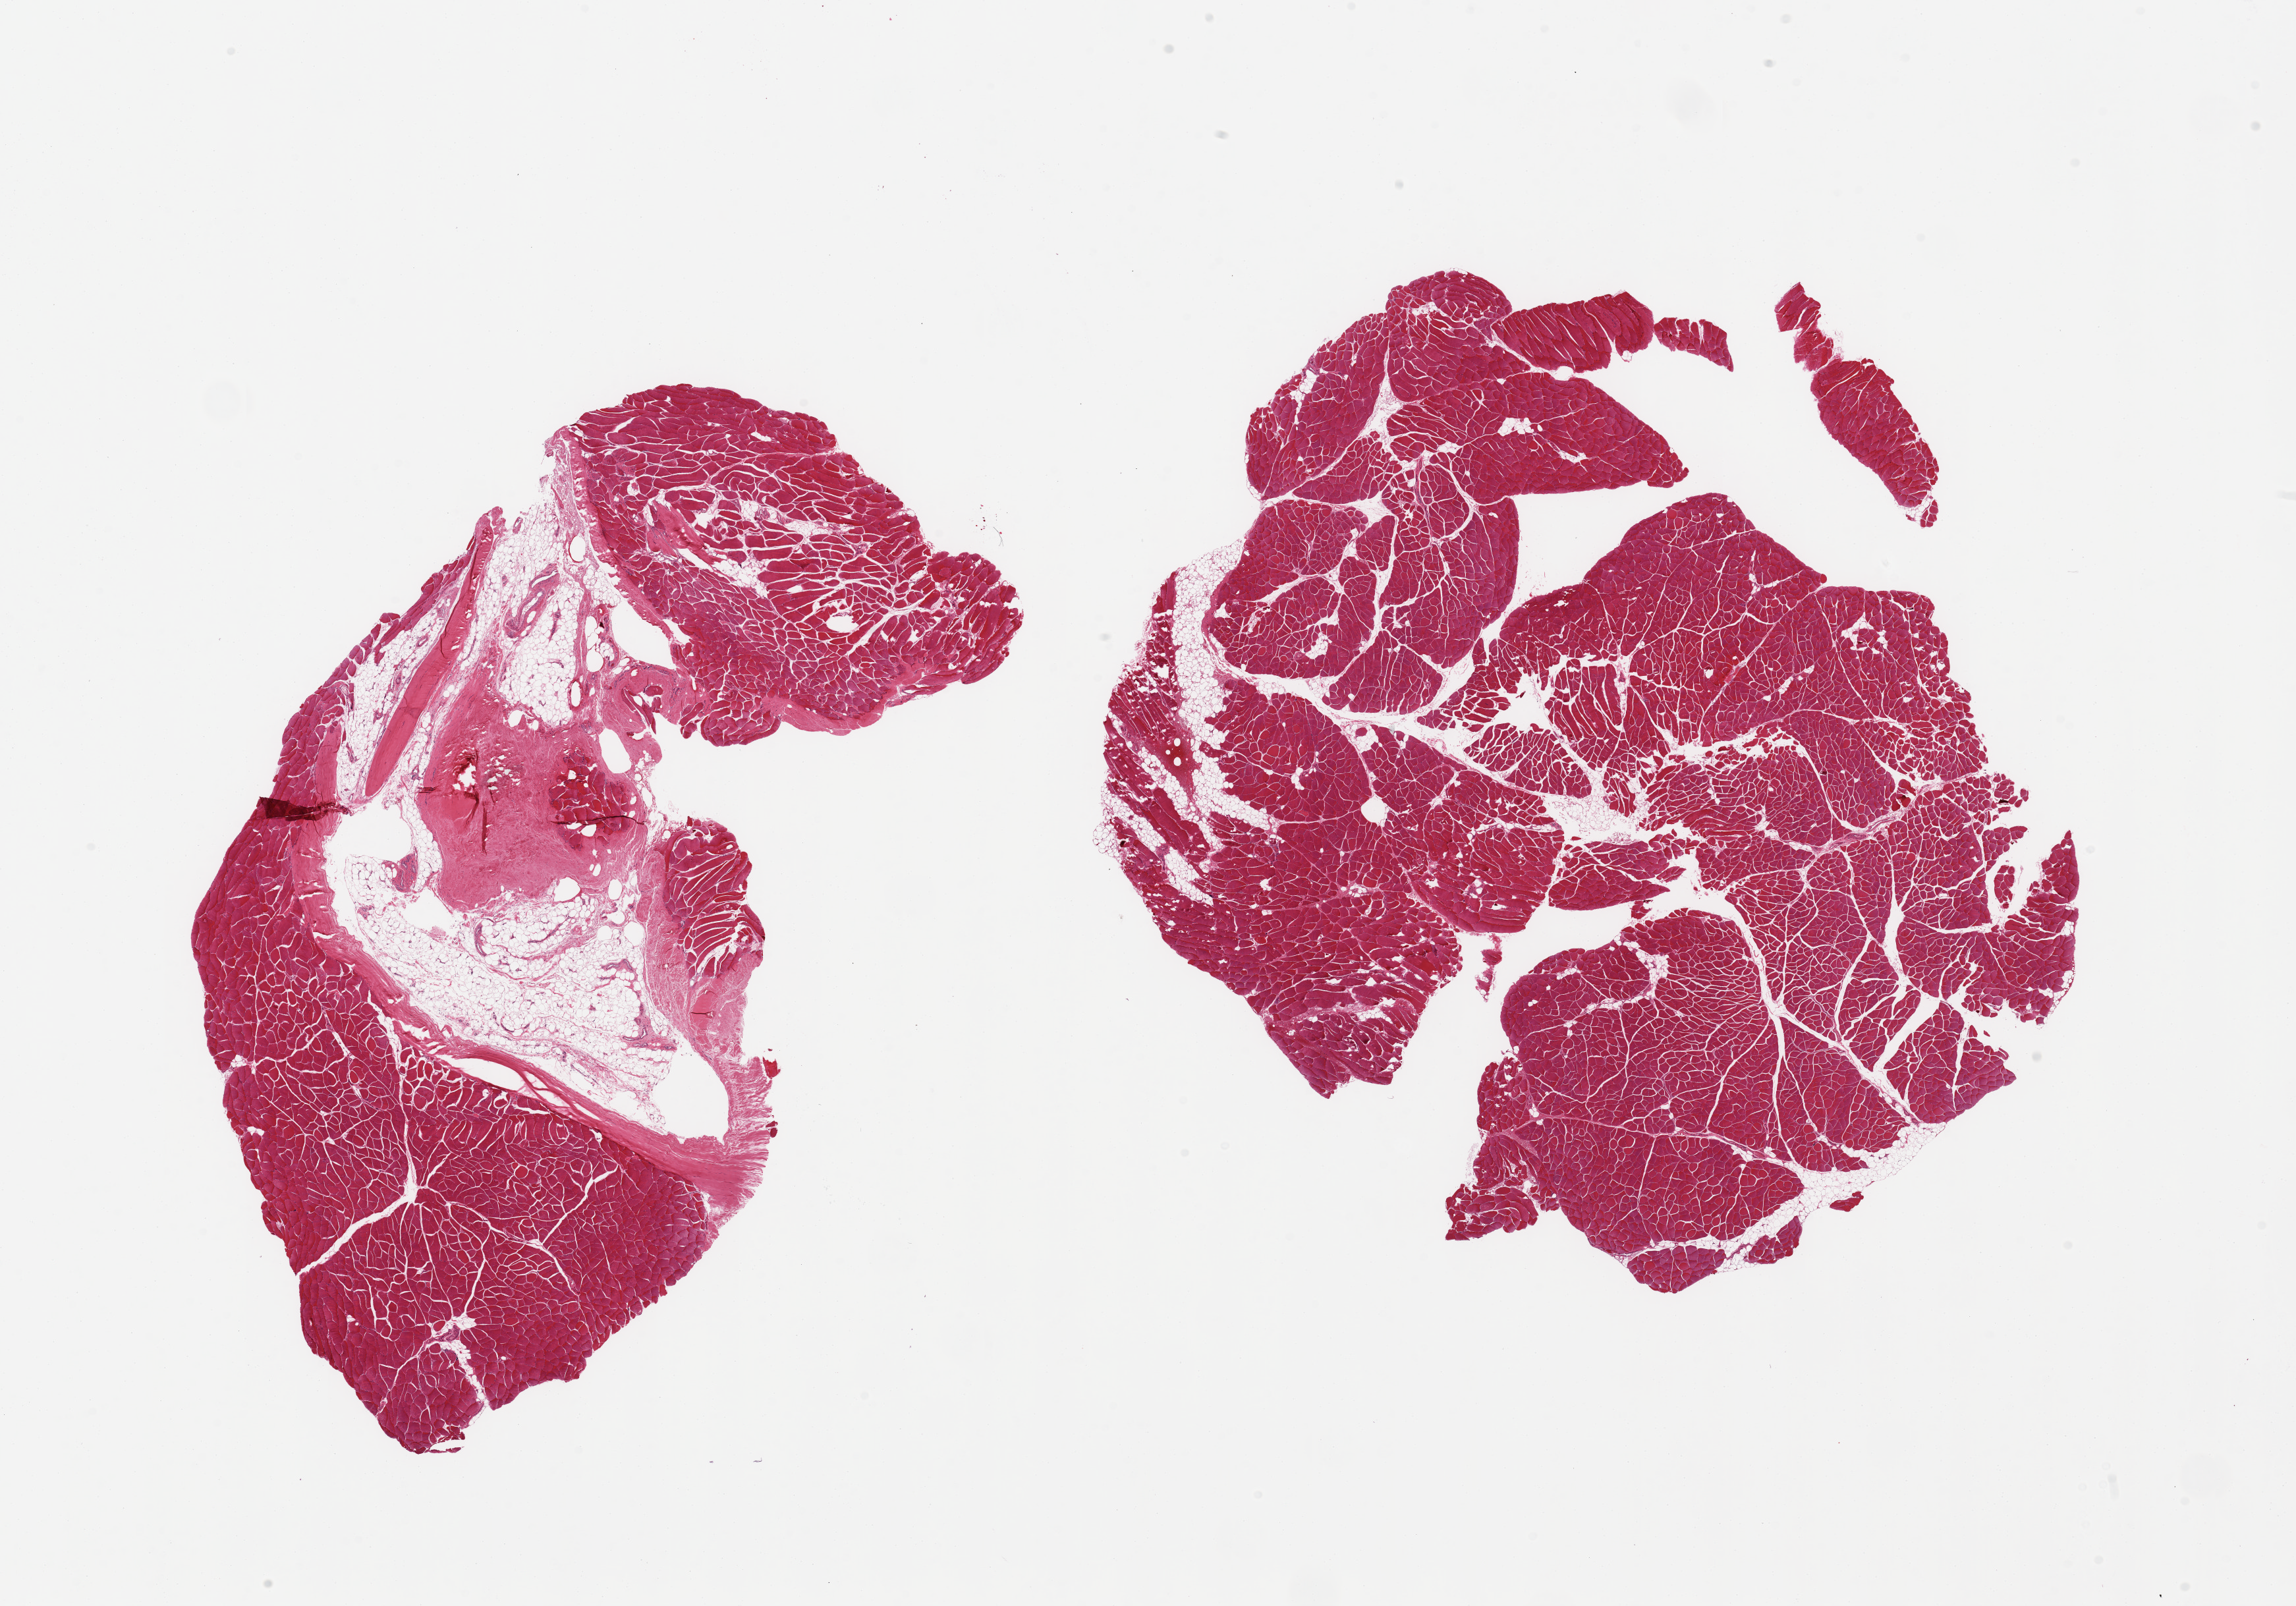
Haematoxylin and eosin whole-slide image, whole scanned area (about 27.6 x 19.3 mm, slide scanned at 20x) shown as a low-resolution overview. PAXgene-fixed paraffin-embedded (PFPE) section. Section of skeletal muscle (target tissue). Donor tissue sample.
Pathologist's review note for this sample: 2 pieces, 1 with 5% fat; other with 40% fat and fibrous content.